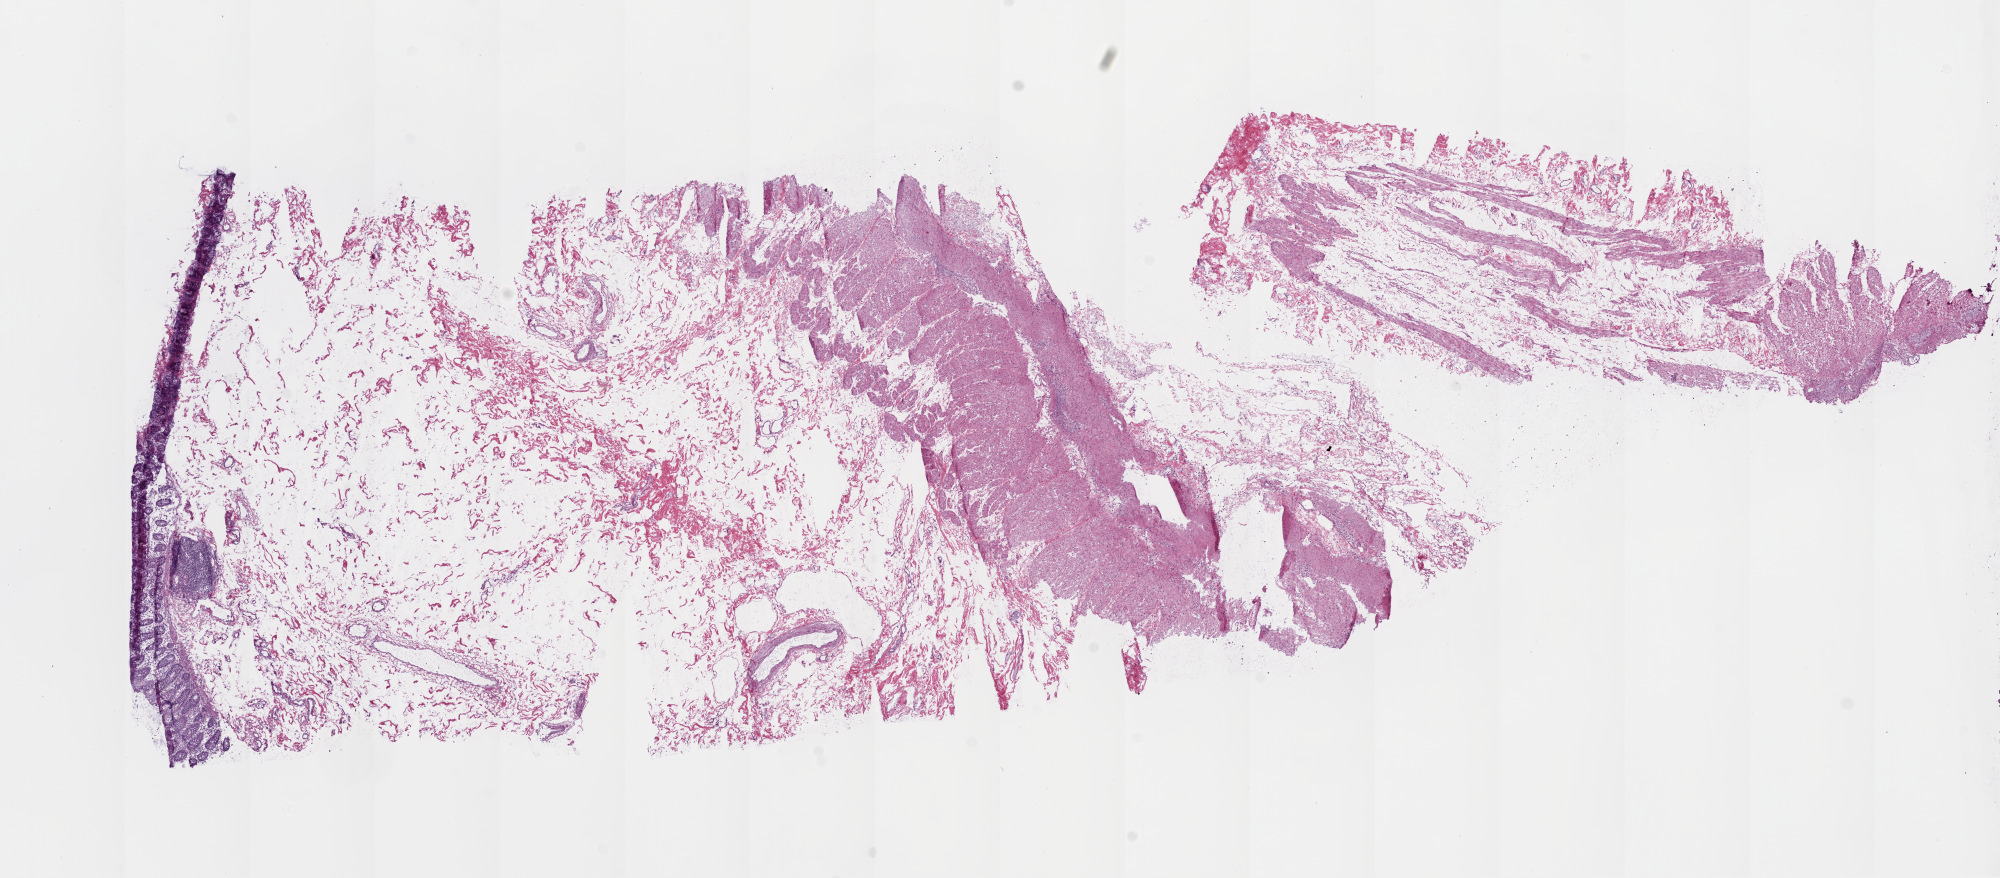
Whole-slide histology image, H&E, whole scanned area (about 16.0 x 7.0 mm, slide scanned at 20x) shown as a low-resolution overview, frozen section, solid tissue normal (non-tumour tissue) sample from the colon. Female, age 75 years at initial diagnosis.
This section: solid tissue normal sample (biorepository sample class). Patient diagnosis: Adenocarcinoma, NOS.